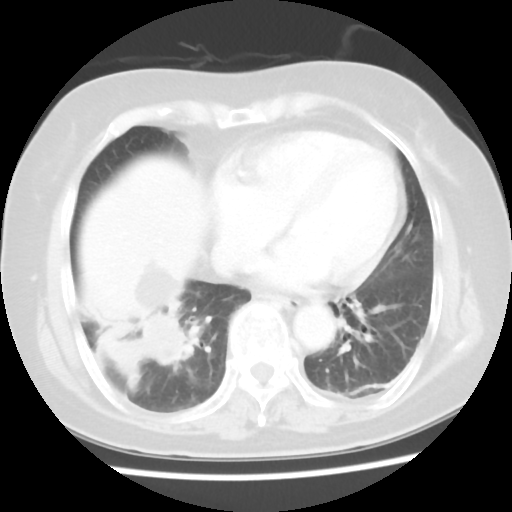
Chest CT, one axial slice; position 14 of 45 along the scan axis; lung window (W 1500 / L -600 HU); 5 mm slice thickness; 512 × 512 image matrix, field of view 312 × 312 mm. Patient: female, 65 years. Case-level facts recorded for this patient, not image findings: clinical TNM (as recorded): T2 N3 M0.
Structures marked on this image (bounding box drawn by a radiologist):
- lung tumour (recorded histology: adenocarcinoma): box from (x=129, y=301) to (x=202, y=376) px